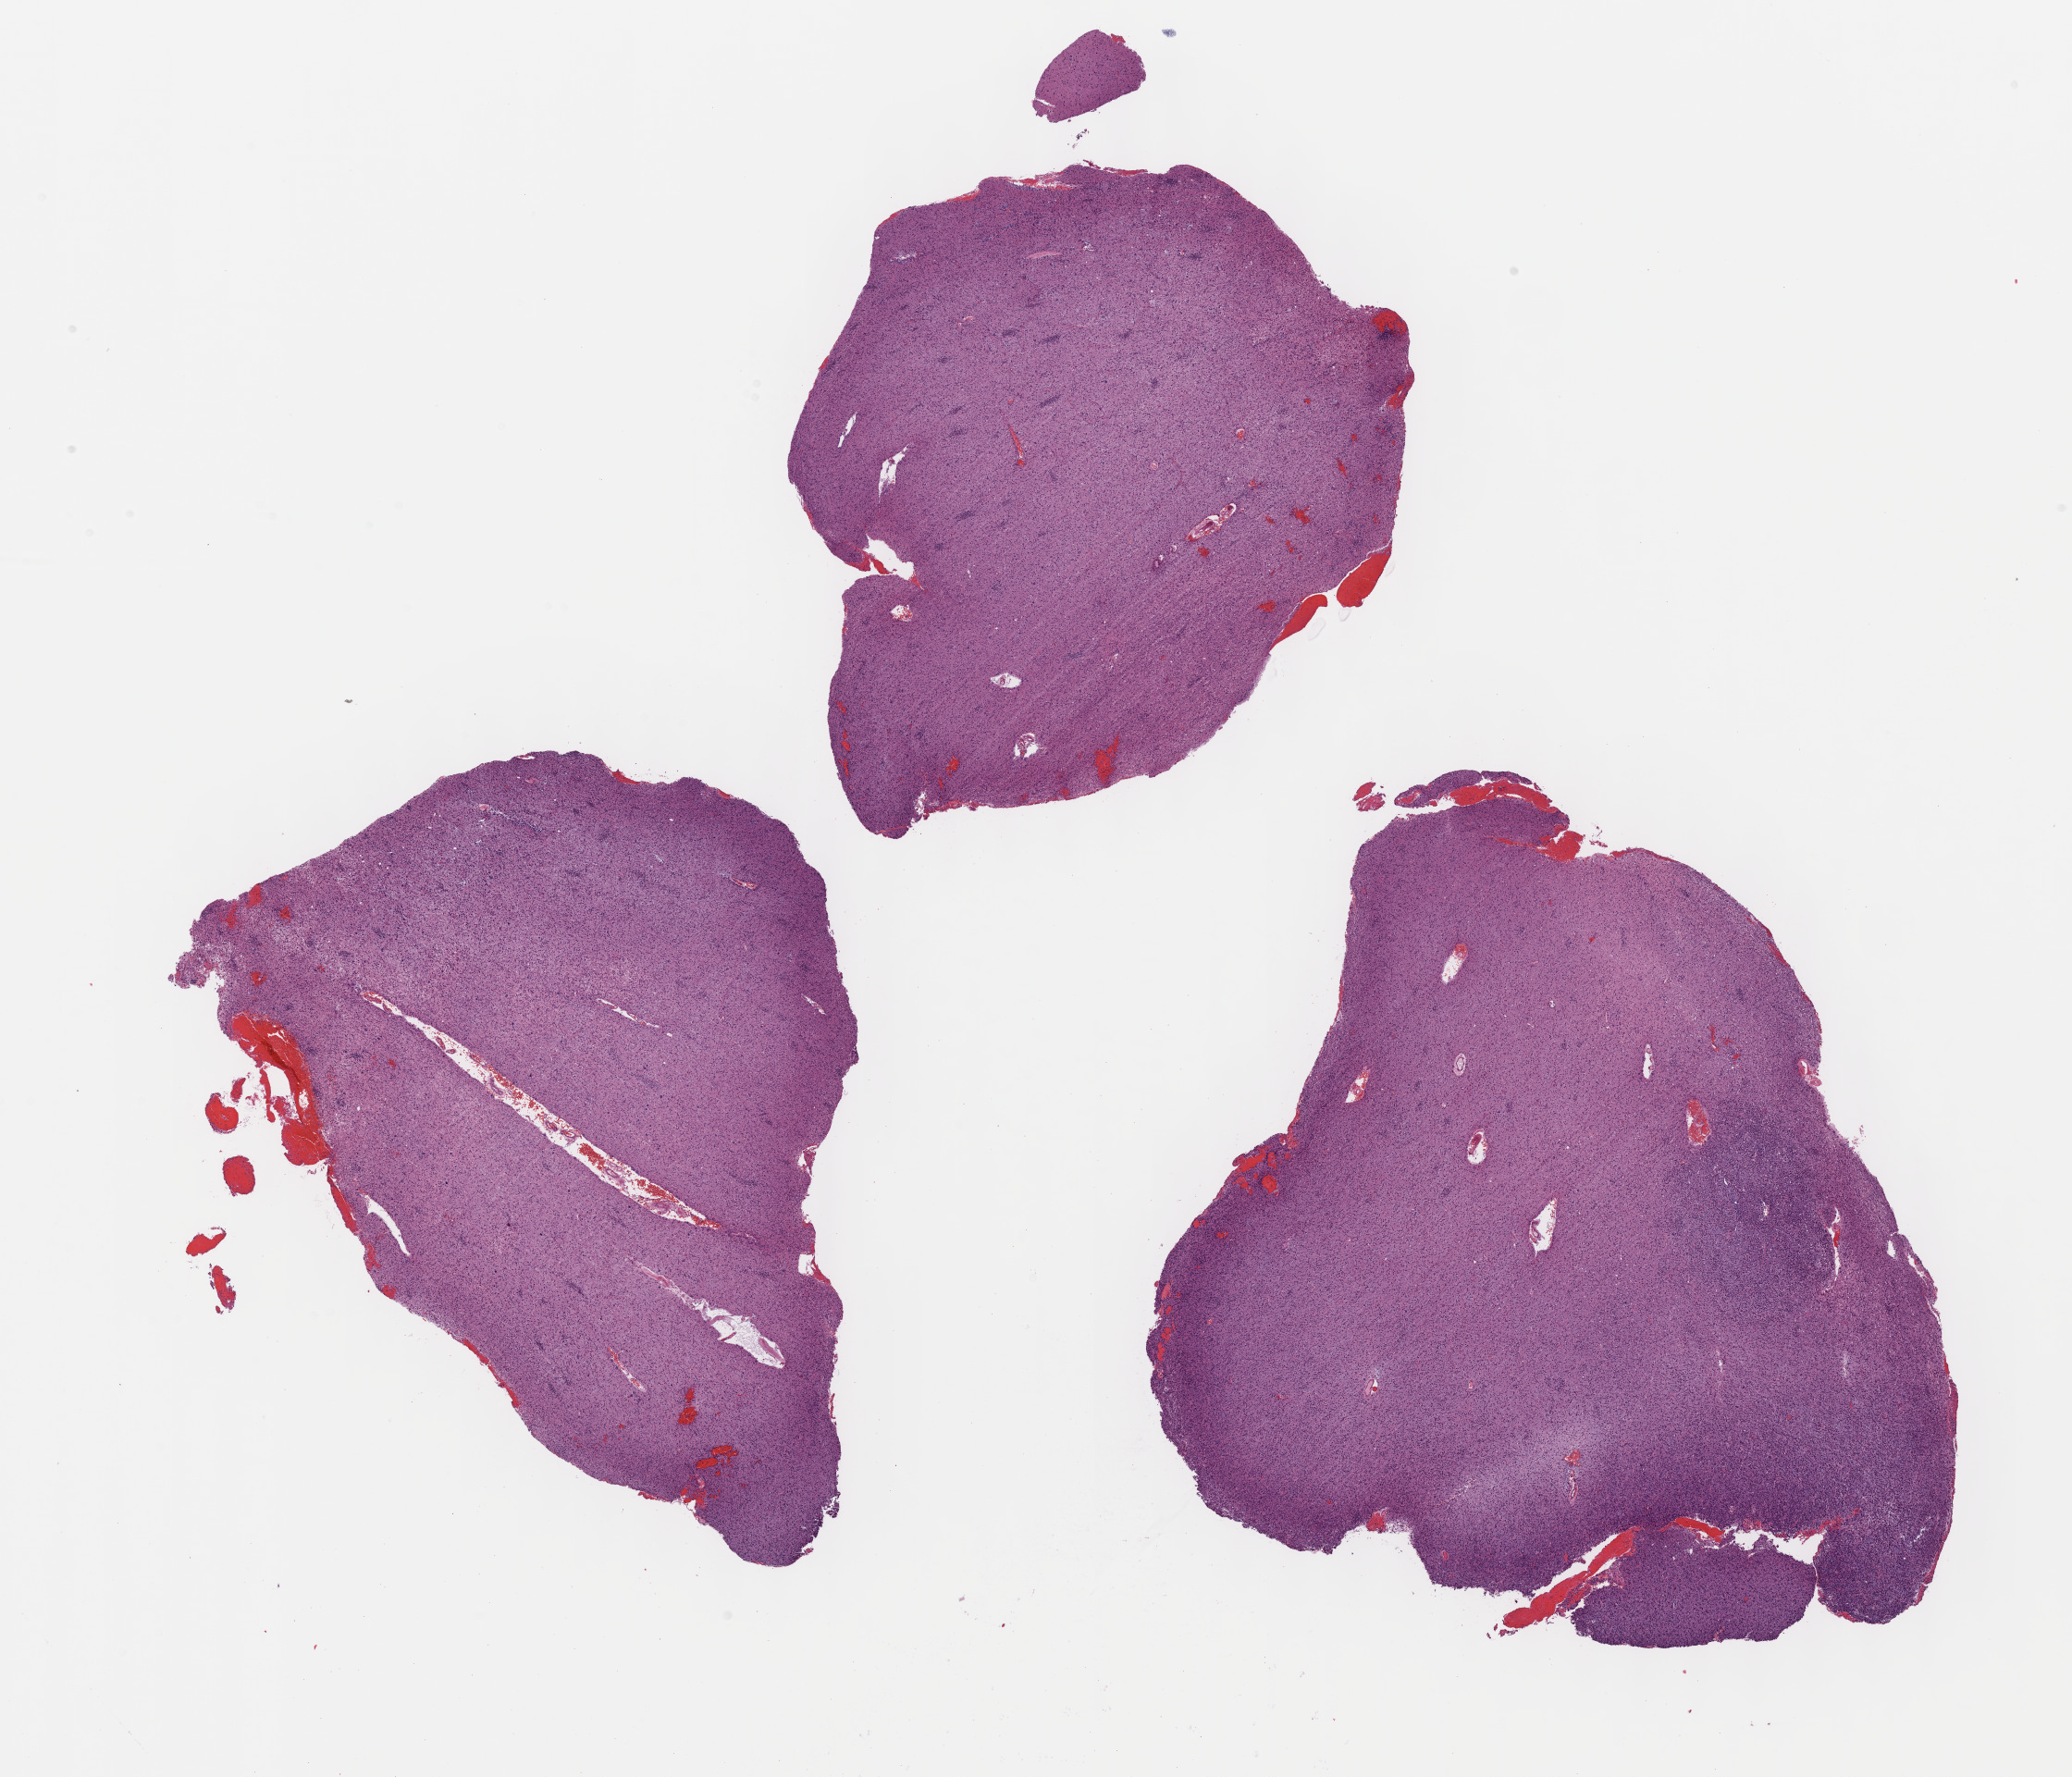
H&E-stained whole-slide image, whole scanned area (about 18.1 x 15.5 mm, from a 40x scan) shown as a low-resolution overview; formalin-fixed paraffin-embedded (FFPE) diagnostic section; brain, primary tumour sample. Male, age 67 years at initial diagnosis. Histologic grade: G3 (poorly differentiated).
* histologic diagnosis: Mixed glioma
* laterality: right